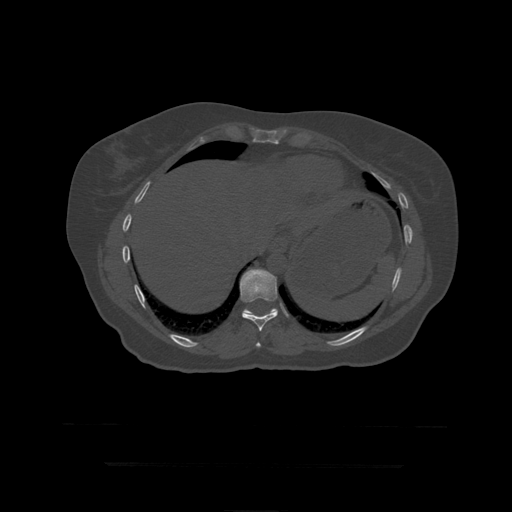
CT including the spine, one axial slice. Slice 237 of 399 in the series (ordered by position). Bone window (W 1800 / L 400 HU). 512 × 512 image matrix, field of view 450 × 450 mm. Patient age 41 years. From the clinical record (not read from this slice): primary cancer: breast.
Annotated regions visible in this slice (semi-automatically segmented with operator editing):
- T10 vertebra: bounding box (x1, y1, x2, y2) in pixels: (240, 269, 278, 332)
- T11 vertebra: (240, 288, 278, 314)
- T9 vertebra: (256, 342, 261, 348)